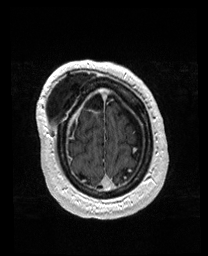
Brain MRI from a brain-tumour surgery series, one axial slice; position 35 of 176 along the scan axis; T1-weighted post-contrast; 1 mm slice thickness; 208 × 256 image matrix, field of view 208 × 256 mm. Case-level facts recorded for this patient, not image findings: histopathology: Astrocytoma; WHO grade: 4; IDH mutation: yes; tumour location: Right Orbitofrontal Anterior Temporal Insular.
Outlined on this slice (outlined manually by an expert reader):
- previous resection cavity: bounding box (x1, y1, x2, y2) in pixels: (56, 90, 106, 109)